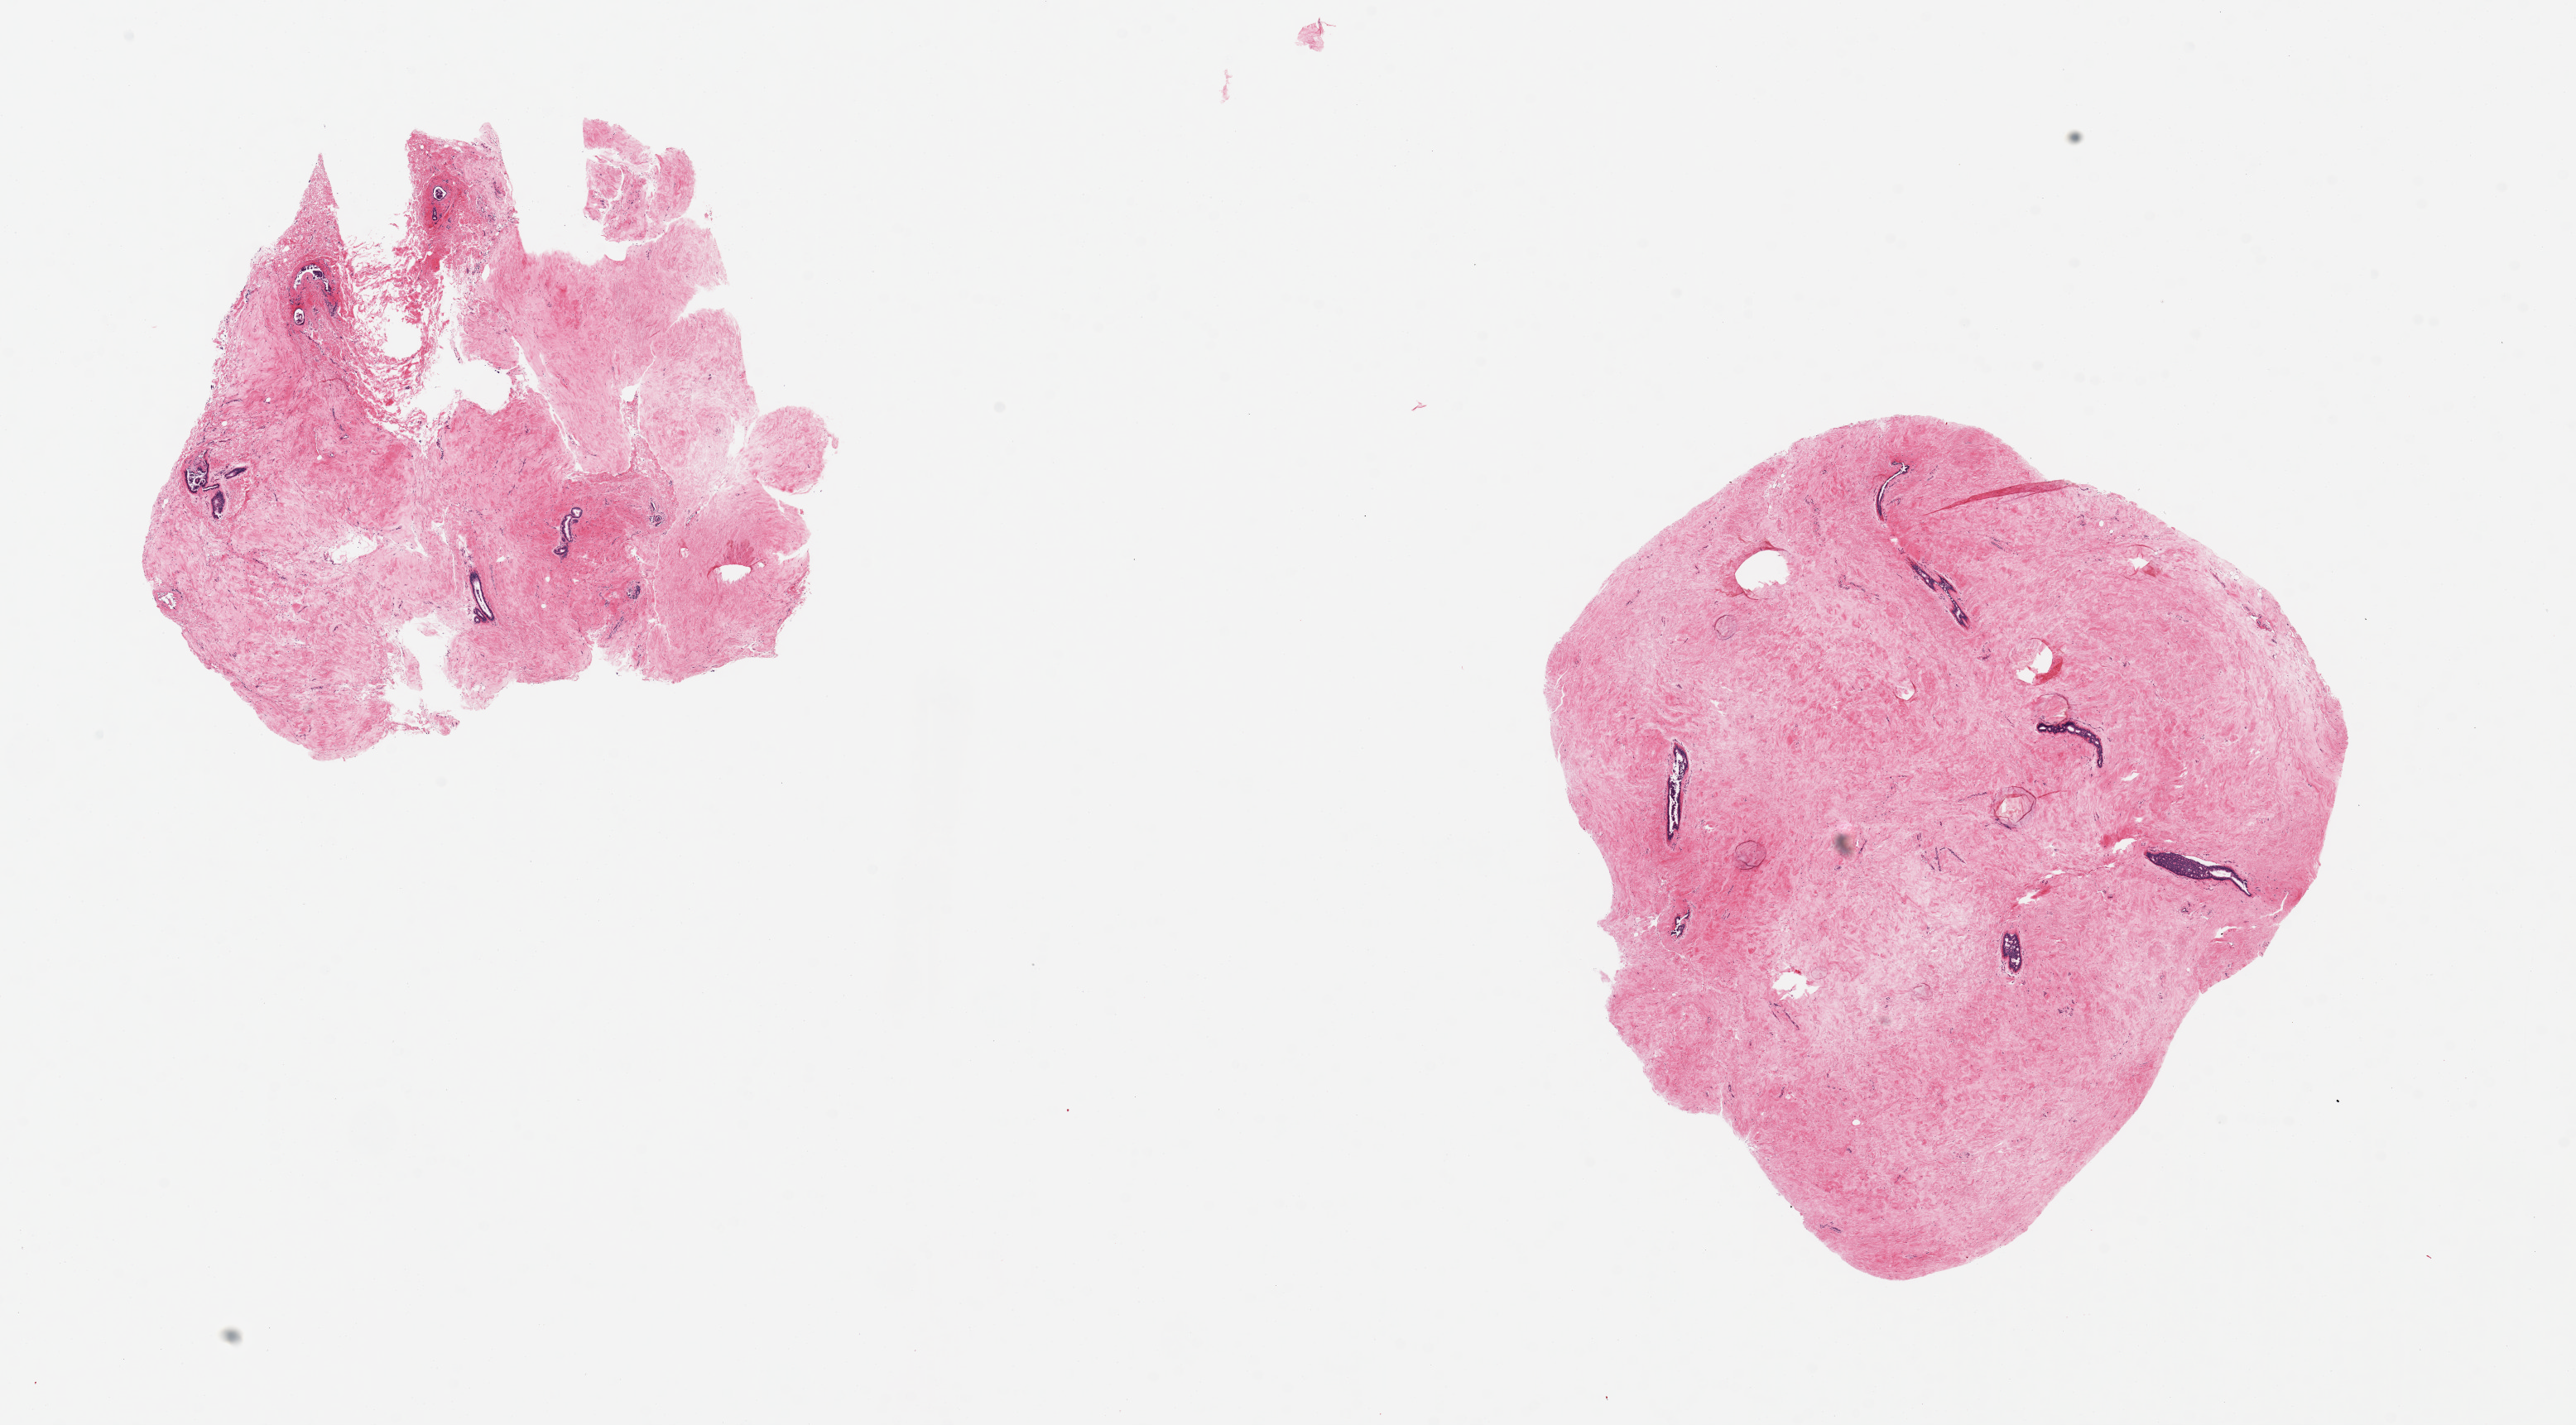
Whole-slide image, hematoxylin and eosin (H&E) stain, whole scanned area (about 24.6 x 13.6 mm) shown as a low-resolution overview. PAXgene-fixed paraffin-embedded (PFPE) section. Target tissue: breast. Tissue donor sample.
• reviewer comment on this tissue sample: 2 pieces, 7x6 & 7.5x7mm; gynecomastia with typical dense stromal hyalinization intraductal papillary hyperplasia